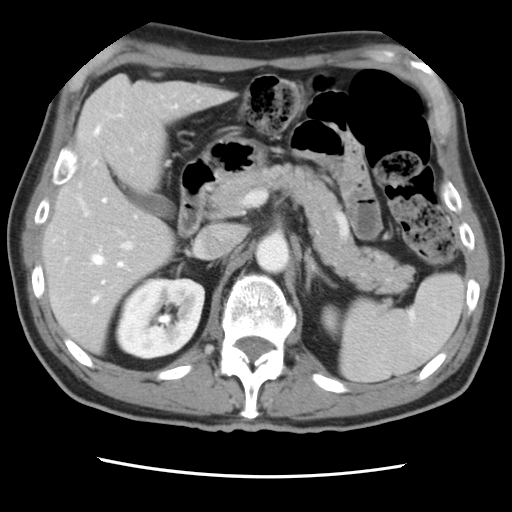
Contrast-enhanced abdominal CT, one axial slice. Position 46 of 83 along the scan axis. 120 kVp. Intravenous contrast given. Soft-tissue window (W 400 / L 40 HU). 5 mm slice thickness. 512 × 512 image matrix, field of view 321 × 321 mm. Male patient, age 69 years. Case-level facts recorded for this patient, not image findings: diagnosis: colorectal cancer liver metastases, imaged before liver resection; multiple liver metastases: yes; largest metastasis: 3.5 cm.
Annotated regions visible in this slice (outlined manually by an expert reader):
- hepatic veins: bounding box <91,105,177,302> (left, top, right, bottom; pixels)
- liver: <45,77,229,350>
- planned liver remnant (the part of the liver to remain after resection): <44,140,175,350>
- portal vein (with intrahepatic branches): <65,184,134,262>